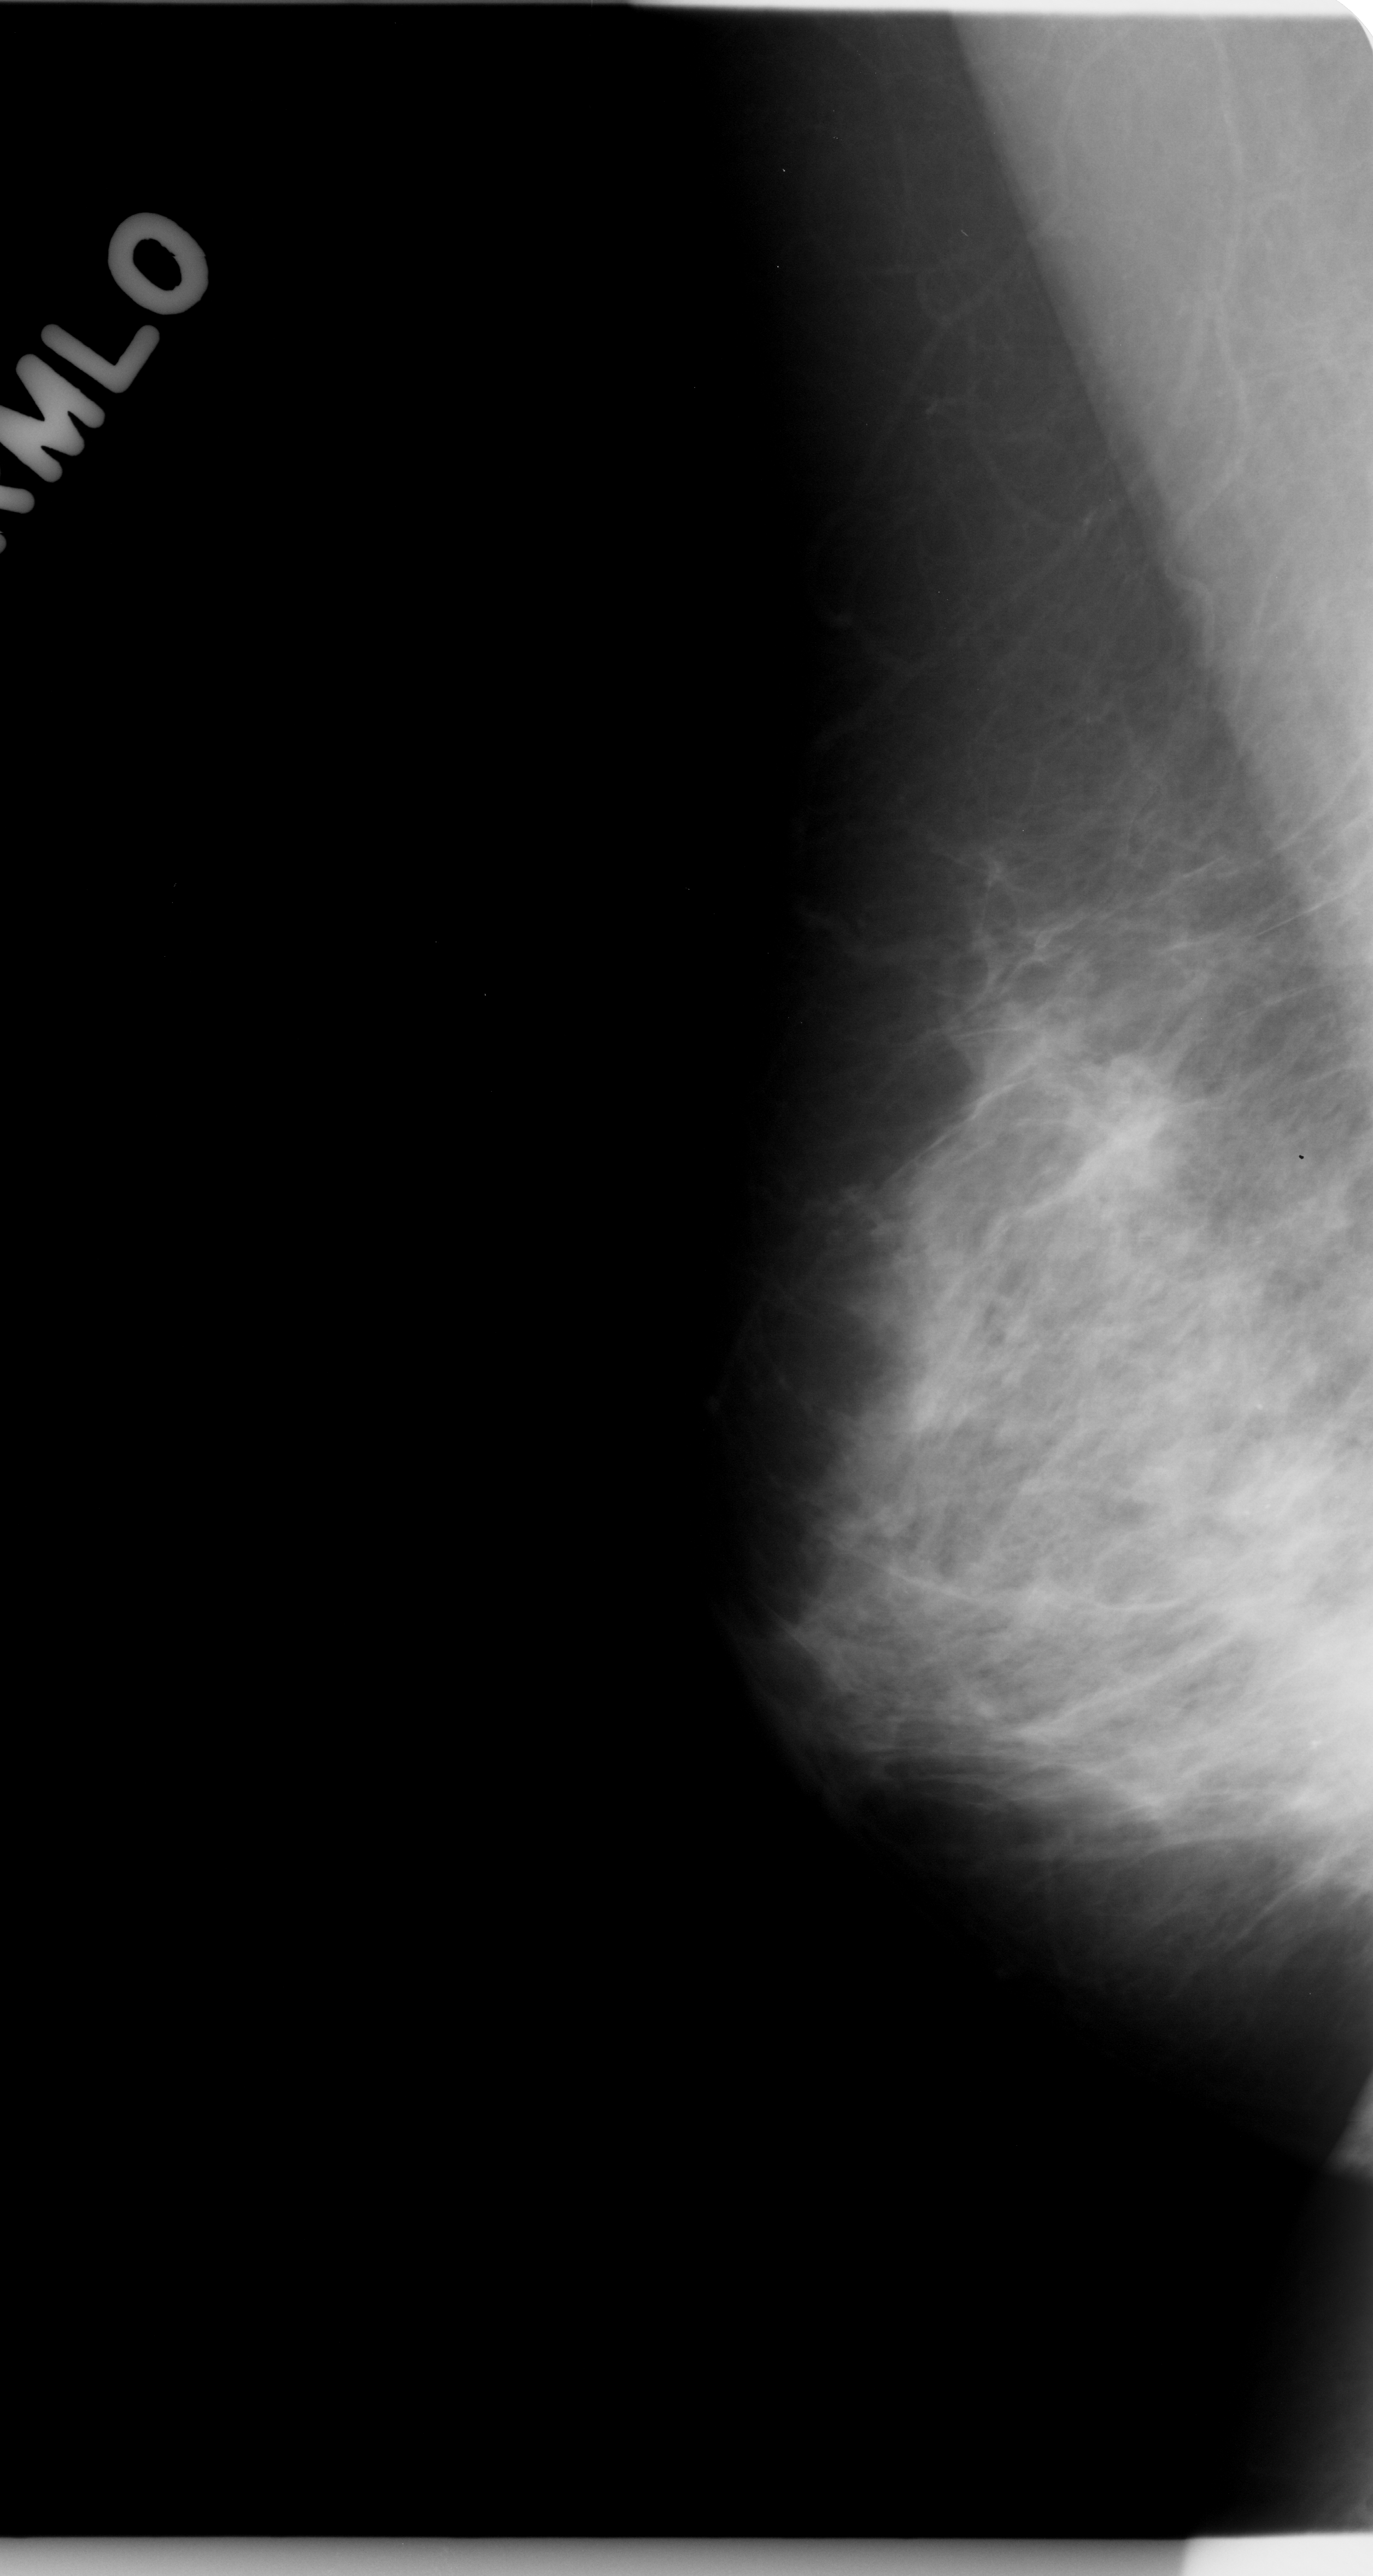
Scanned film-screen mammogram, right breast, MLO view, breast composition: heterogeneously dense (BI-RADS density category 3 of 4).
Abnormality record for this image: mass, shape irregular, margins ill defined; BI-RADS assessment category 4; pathology (as recorded): malignant.